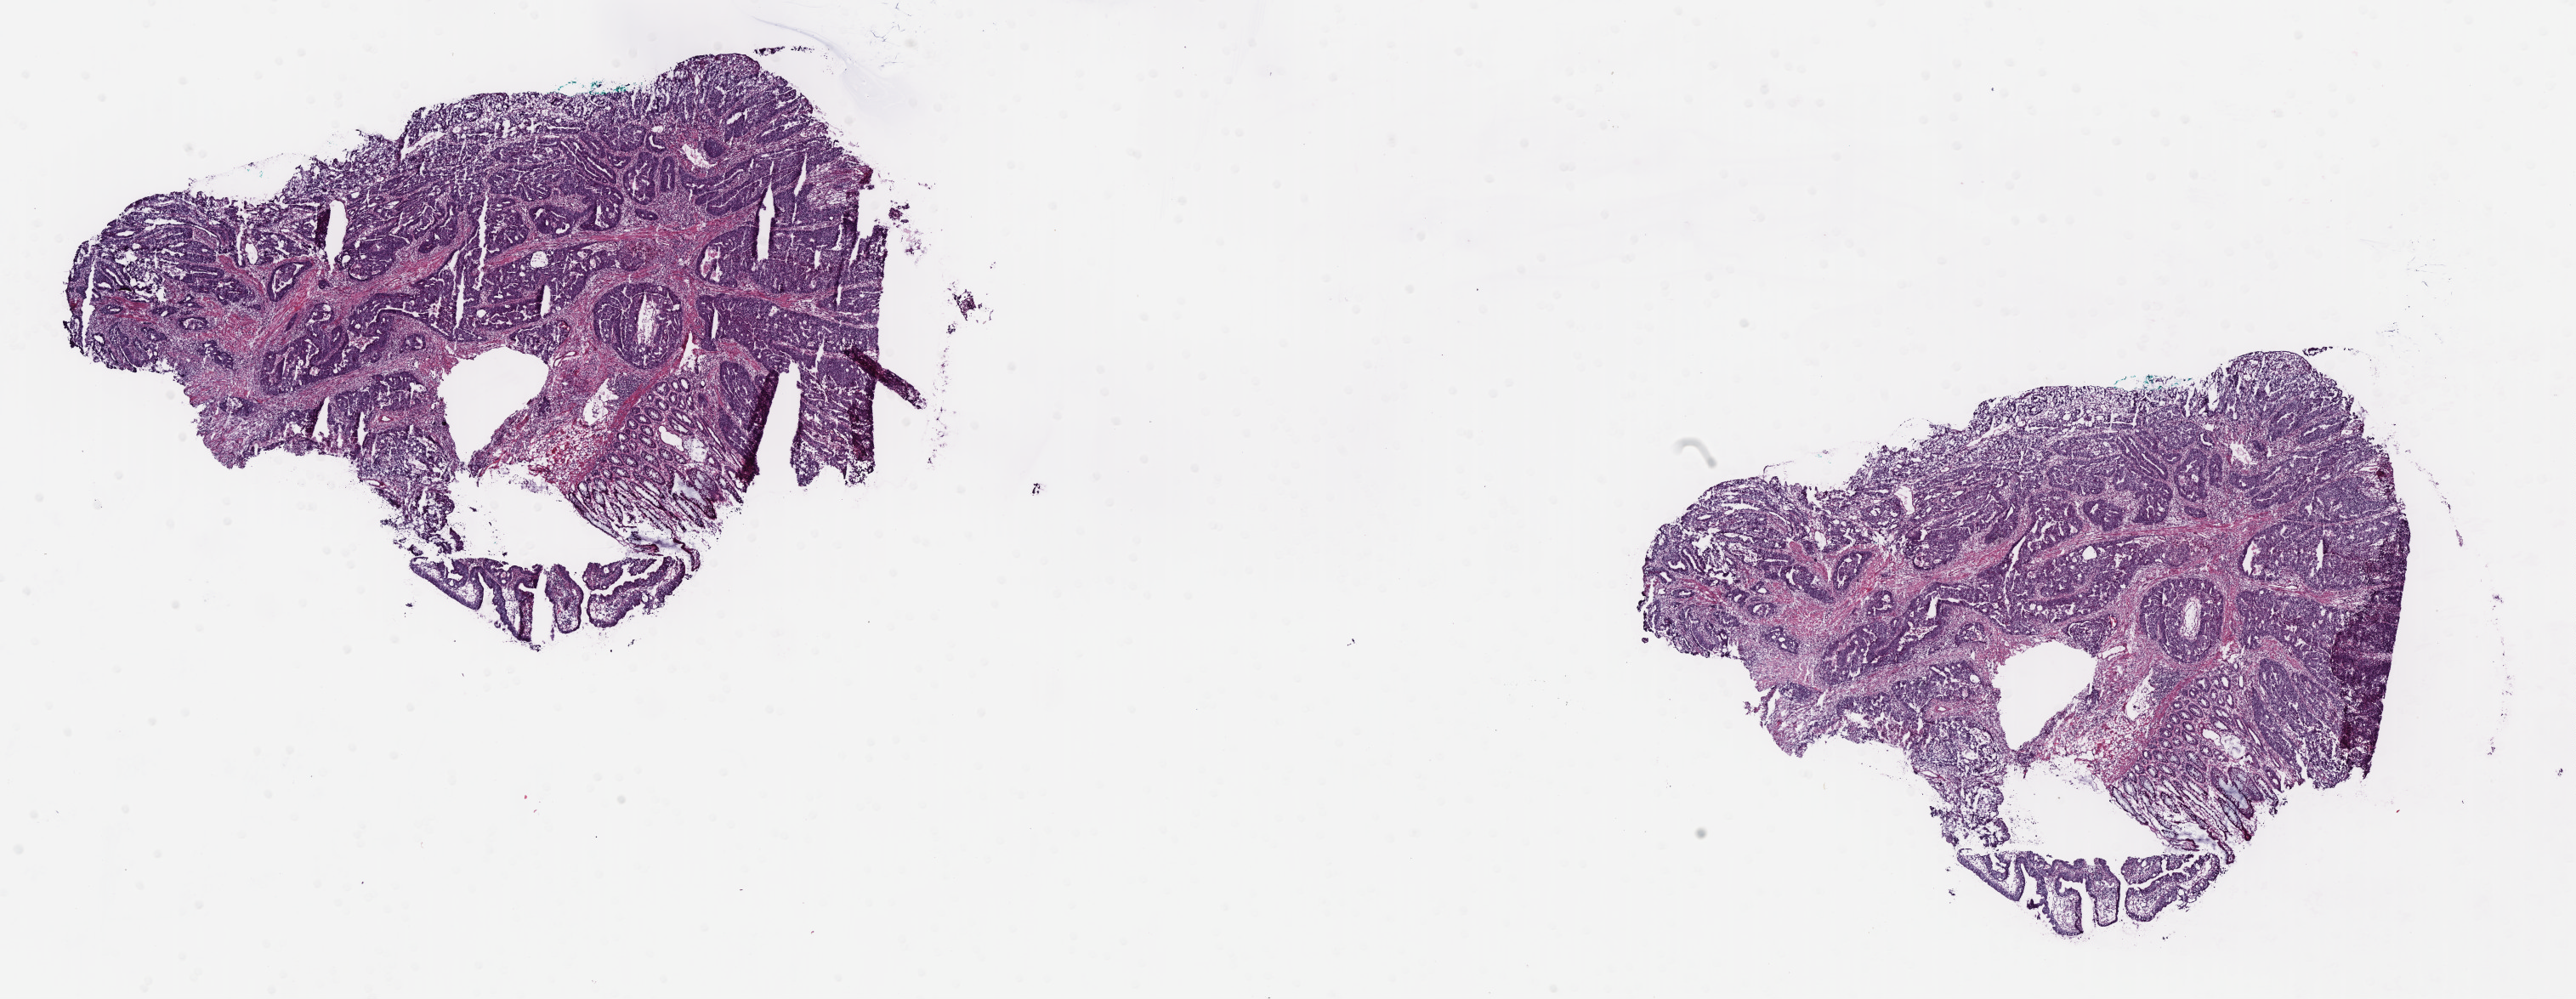
Whole-slide histology image, Hematoxylin and eosin (H&E) stained — a low-resolution overview of the entire scanned area, about 24.3 x 9.4 mm (from a 40x scan), frozen section from the bottom of the tissue portion, rectum, primary tumour sample. Female, age 68 years at initial diagnosis. Slide review estimates, as recorded: tumour cells 85%, tumour nuclei 80%, normal cells 10%, stromal cells 4%, necrosis 1%. Infiltration values recorded for this section: lymphocyte infiltration 2%, monocyte infiltration 2%, neutrophil infiltration 3%.
Lymph nodes positive (case pathology): 0 of 23 examined. Histologic diagnosis: Adenocarcinoma, NOS. AJCC pathologic stage: IV (6th edition).